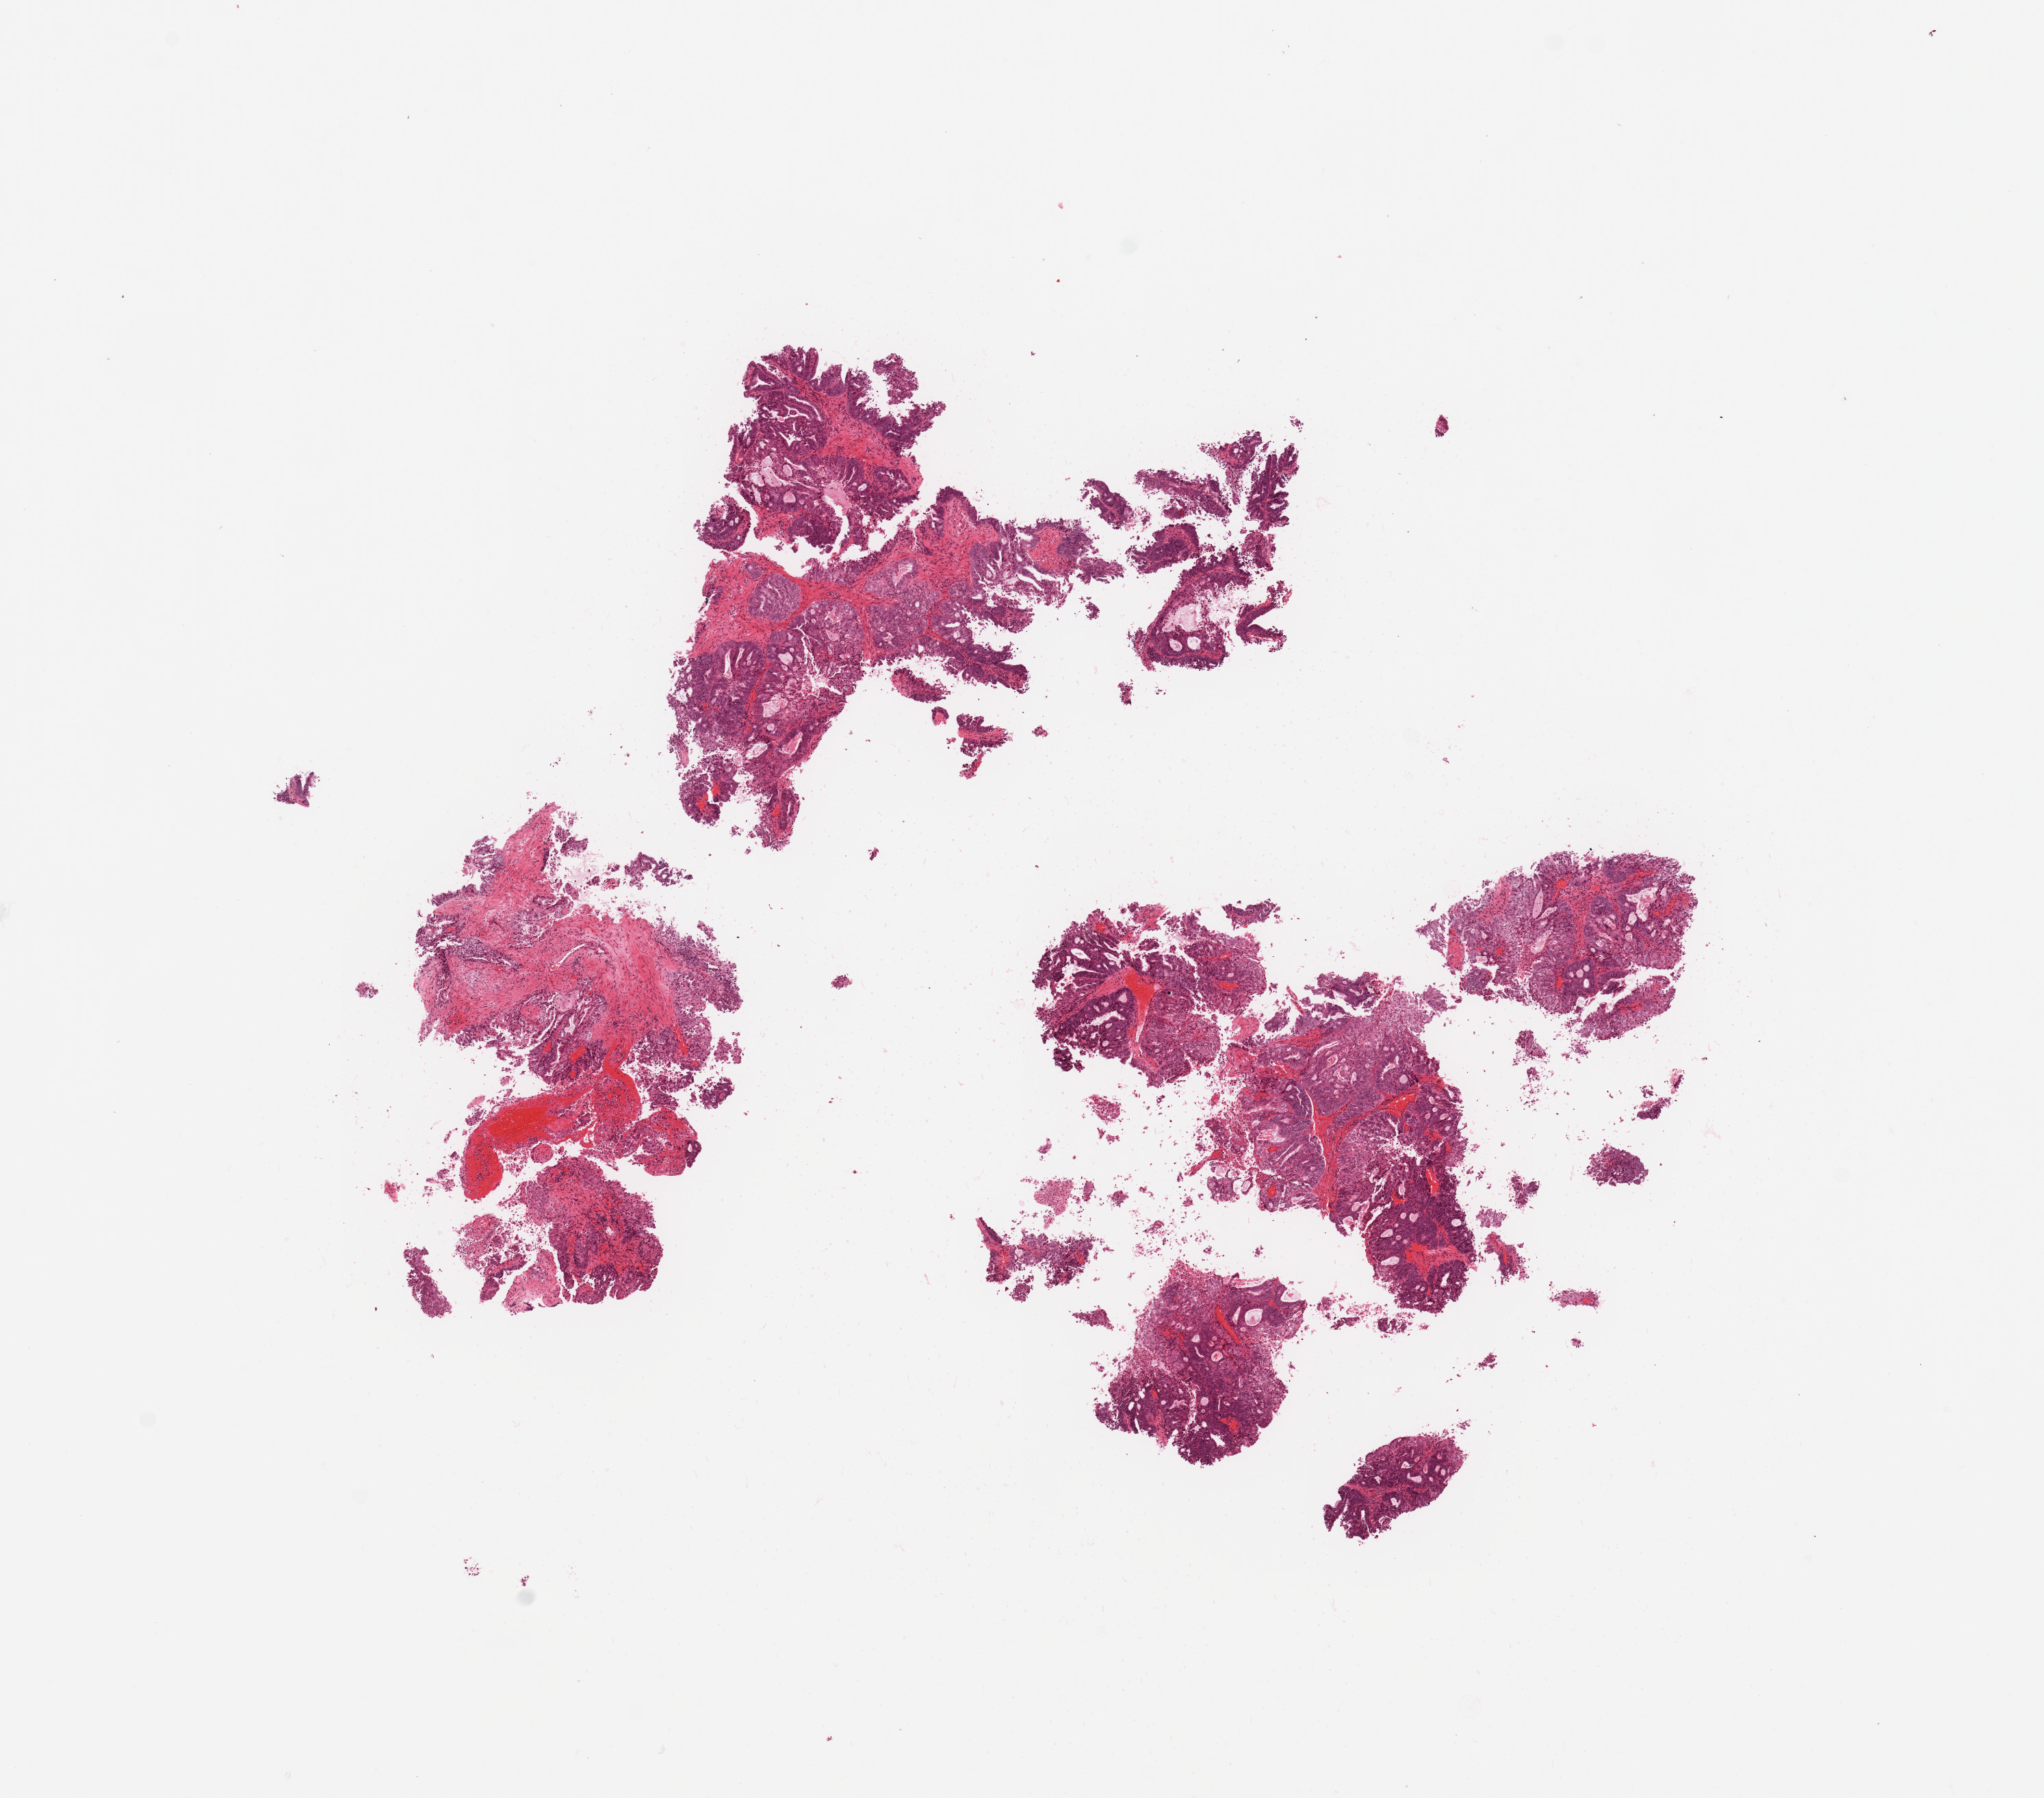
Digitized H&E-stained tissue section (whole slide), shown as a low-resolution overview of the whole scanned area (about 11.8 x 10.4 mm, from a 20x scan); tumour tissue sample, uterus. 59-year-old female patient. Histologic grade: G2 (moderately differentiated).
* AJCC pathologic stage: IA
* histologic diagnosis: Endometrioid adenocarcinoma, NOS